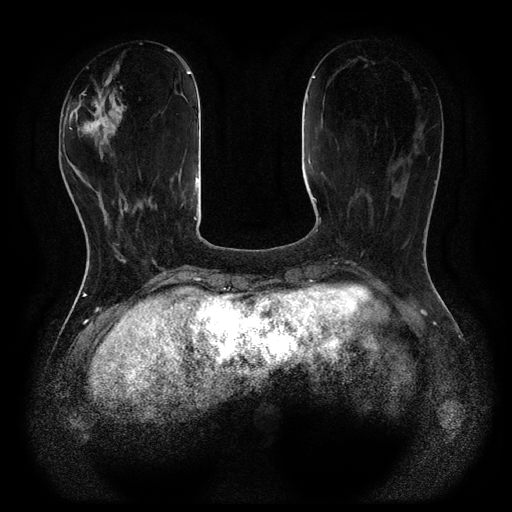
Breast MRI (dynamic contrast-enhanced, multi-phase), one axial slice. Dynamic contrast-enhanced series, time point 2 of 5 at this slice position (early post-contrast). 1.5 T. TE 2.6 ms, TR 5.4 ms. 2 mm slice thickness. 512 × 512 image matrix, field of view 340 × 340 mm. Patient: female, 48 years.
Structures marked on this image (semi-automatically segmented with operator editing):
- breast lesion (labelled benign in the annotation): bounding box (x1, y1, x2, y2) in pixels: (70, 55, 128, 160)